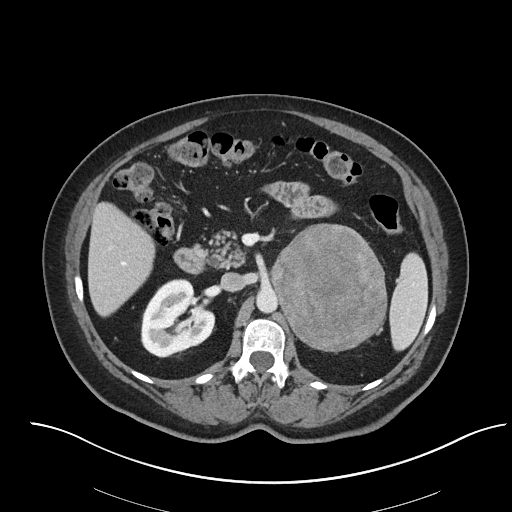
Contrast-enhanced abdominal CT, one axial slice; position 42 of 92 along the scan axis; reconstruction kernel I40f/2; soft-tissue window (W 400 / L 40 HU); 3 mm slice thickness; 512 × 512 image matrix, field of view 440 × 440 mm. Patient: female, 53 years. From the clinical record (not read from this slice): diagnosis: adrenocortical carcinoma; tumour side: left adrenal; tumour size at pathology: 9 cm; Ki-67 index: 28 %; stage (as recorded): 2.
Outlined on this slice (semi-automatically segmented with operator editing):
- mass: bounding box <271,225,386,350> (left, top, right, bottom; pixels)